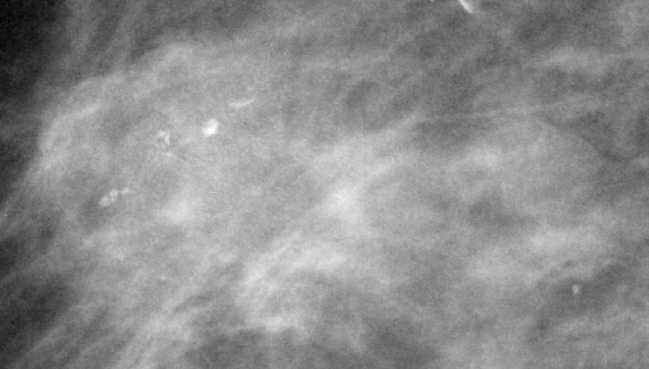
Crop from a digitized film mammogram around one marked abnormality, right breast, MLO view.
Calcifications, morphology pleomorphic, distribution clustered; BI-RADS assessment category 4; subtlety rating 3 on a 1 (subtle) to 5 (obvious) scale; pathology result (as recorded, not read from the image): malignant.